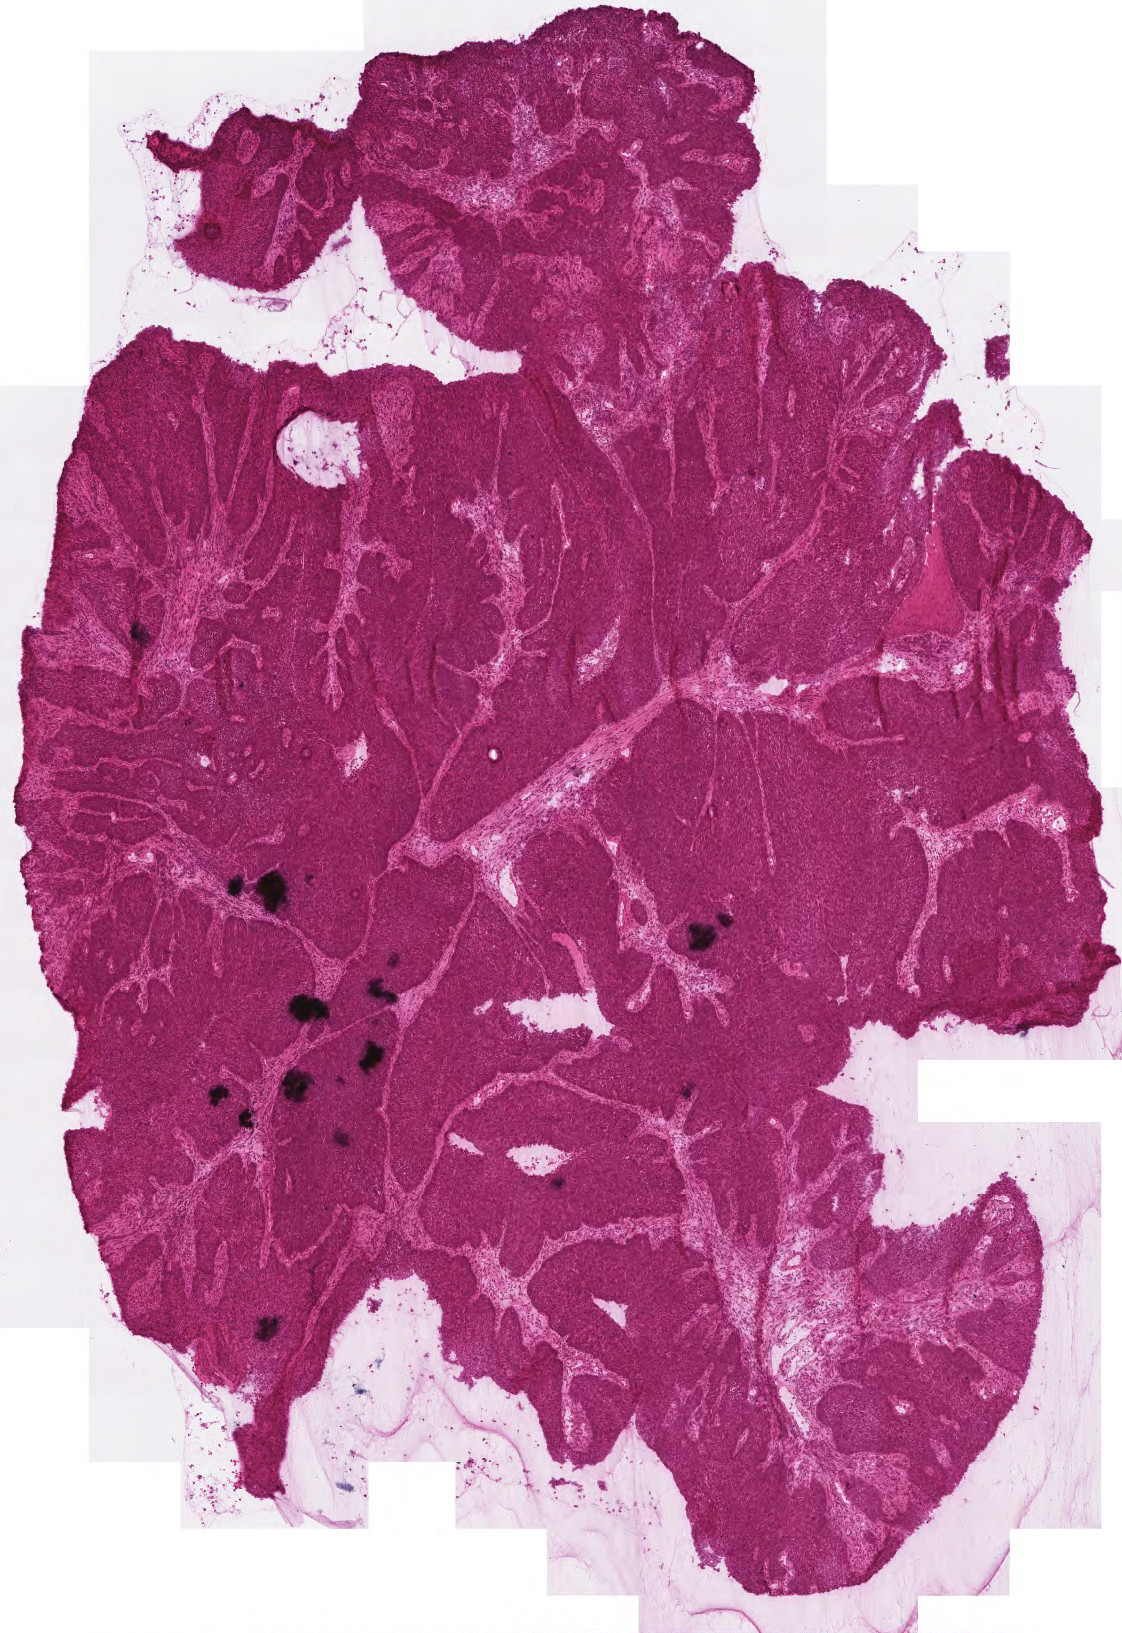
Whole-slide histology image, H&E, shown as a low-resolution overview of the whole scanned area (about 2.2 x 3.3 mm); frozen section; primary tumour sample from the head and neck. Male patient; age at initial diagnosis 68 years. Histologic grade: G3 (poorly differentiated). Composition of this section per pathologist review: tumour cells 90%, tumour nuclei 90%, normal cells 0%, stromal cells 10%, necrosis 0%.
- diagnosis: Squamous cell carcinoma, NOS (hypopharynx, NOS)
- laterality: left